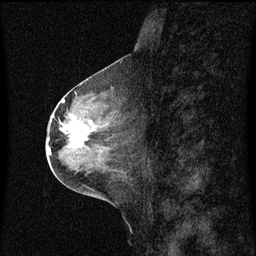
Breast MRI (dynamic contrast-enhanced), one sagittal slice. Position 30 of 60 along the scan axis. Dynamic contrast-enhanced series, image 2 of 3 at this slice position (ordered by acquisition). 1.5 T. TE 4.2 ms, TR 8.4 ms. 2 mm slice thickness. 256 × 256 image matrix, field of view 200 × 200 mm. Female patient, age 49 years. From the clinical record (not read from this slice): setting: breast cancer imaged before/during neoadjuvant chemotherapy; receptor status: HR-positive, HER2-negative.
Annotated regions visible in this slice (semi-automatically segmented with operator editing):
- analysis volume of interest (the breast-tissue region the enhancement analysis was run in; not a lesion): bounding box <59,101,116,158> (left, top, right, bottom; pixels)
- tumour enhancement mask (voxels above the 70 % enhancement threshold inside the analysis volume of interest): <66,121,92,148>